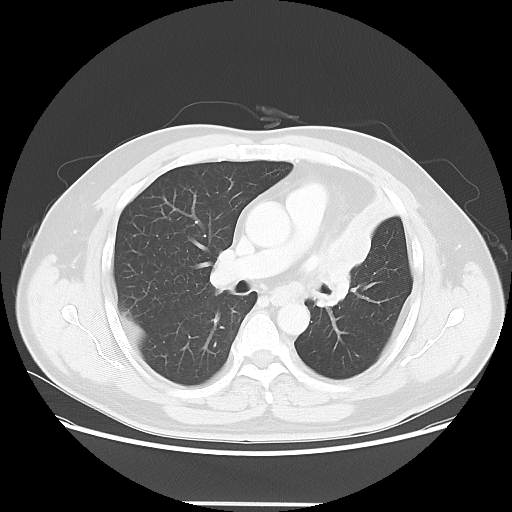
Chest CT, one axial slice; slice 36 of 62 in the series (ordered by position); reconstruction kernel LUNG; 120 kVp; lung window (W 1500 / L -600 HU); 5 mm slice thickness; 512 × 512 image matrix, field of view 403 × 403 mm. Patient: male, 49 years. Case-level facts recorded for this patient, not image findings: clinical TNM (as recorded): T3 N3 M1c.
Structures marked on this image (bounding box drawn by a radiologist):
- lung tumour (recorded histology: squamous cell carcinoma): bounding box (x1, y1, x2, y2) in pixels: (314, 227, 387, 312)